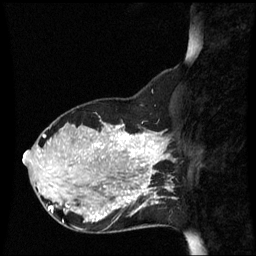
Breast MRI (dynamic contrast-enhanced), one sagittal slice. Slice 20 of 60 in the series (ordered by position). Dynamic contrast-enhanced series, image 2 of 3 at this slice position (ordered by acquisition). 1.5 T. TE 4.2 ms, TR 8.9 ms. 2.2 mm slice thickness. 256 × 256 image matrix. Female patient, age 31 years. From the clinical record (not read from this slice): setting: breast cancer imaged before/during neoadjuvant chemotherapy; receptor status: HR-positive, HER2-negative.
Structures marked on this image (semi-automatic segmentation, software-assisted and operator-edited):
- analysis volume of interest (the breast-tissue region the enhancement analysis was run in; not a lesion): bounding box (x1, y1, x2, y2) in pixels: (90, 180, 152, 233)
- tumour enhancement mask (voxels above the 70 % enhancement threshold inside the analysis volume of interest): (140, 184, 152, 195)